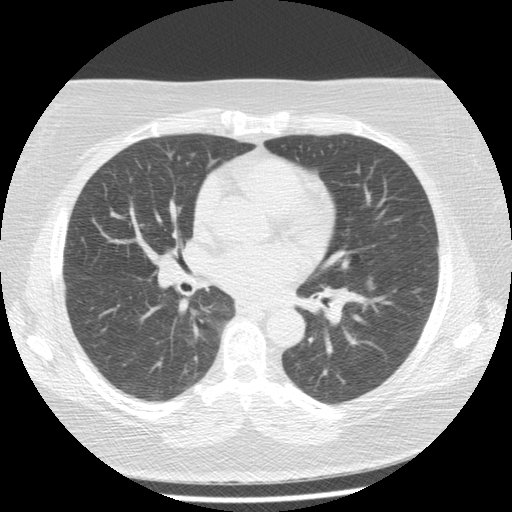
Low-dose screening chest CT, axial slice, second annual screen, lung window (W 1500 / L -600 HU), slice 74 of 157 in the series. Female, age 65 years at enrolment. Current smoker at enrolment.
• Lesion marked by an expert reader, box from (x=352, y=273) to (x=382, y=303) px.
• Screening reader's record for this exam (one nodule recorded; not confirmed to be the boxed lesion): non-calcified nodule or mass ≥4 mm, left lower lobe, 9 × 7 mm, poorly defined margins, soft tissue attenuation, pre-existing on the prior screen: yes; interval growth: yes.
• Official screen result: positive, other.